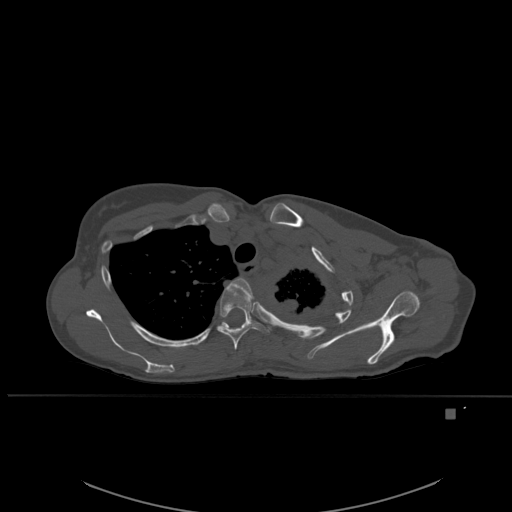
CT including the spine, one axial slice. Position 413 of 537 along the scan axis. Bone window (W 1800 / L 400 HU). 1.5 mm slice thickness. 512 × 512 image matrix, field of view 440 × 440 mm. Patient: female, 45 years. Case-level facts recorded for this patient, not image findings: primary cancer: lung.
Annotated regions visible in this slice (semi-automatic segmentation, software-assisted and operator-edited):
- T3 vertebra: bounding box (x1, y1, x2, y2) in pixels: (230, 278, 253, 302)
- T4 vertebra: (217, 286, 262, 350)
- T5 vertebra: (200, 341, 203, 343)